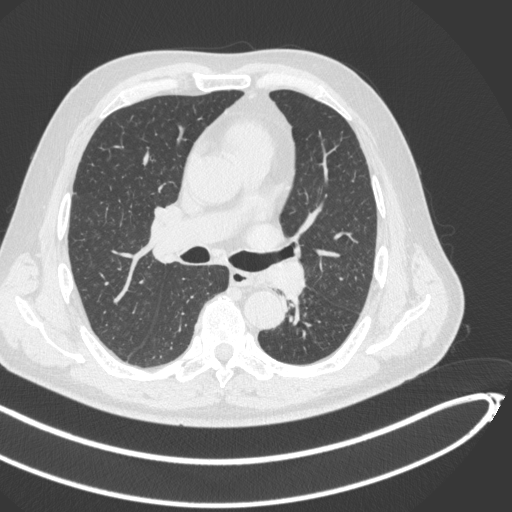
Chest CT, one axial slice. Position 271 of 466 along the scan axis. Lung window (W 1500 / L -600 HU). 1 mm slice thickness. 512 × 512 image matrix, field of view 400 × 400 mm. Patient: male, 64 years. Case-level facts recorded for this patient, not image findings: clinical TNM (as recorded): T1c N0 M0; histopathological grade: G2.
Annotated regions visible in this slice (rectangle marked by the reading radiologist):
- lung tumour (recorded histology: squamous cell carcinoma): bounding box (x1, y1, x2, y2) in pixels: (269, 257, 308, 300)